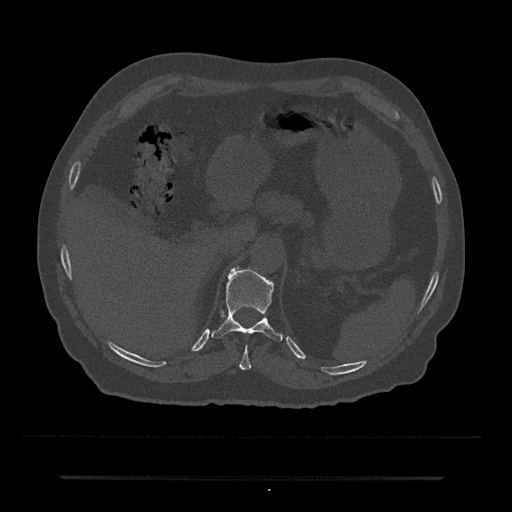
CT including the spine, one axial slice. Slice 185 of 797 in the series (ordered by position). Bone window (W 1800 / L 400 HU). 0.5 mm slice thickness. 512 × 512 image matrix. Male patient, age 69 years. Case-level facts recorded for this patient, not image findings: primary cancer: prostate.
Structures marked on this image (semi-automatic segmentation, software-assisted and operator-edited):
- T10 vertebra: bounding box (x1, y1, x2, y2) in pixels: (239, 345, 252, 370)
- T11 vertebra: (211, 267, 283, 342)